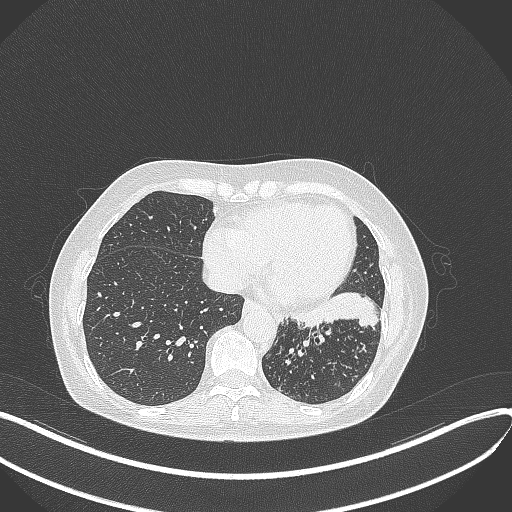
Chest CT, one axial slice. Slice 131 of 429 in the series (ordered by position). Reconstruction kernel B70f. 100 kVp. Lung window (W 1500 / L -600 HU). 1 mm slice thickness. 512 × 512 image matrix. Patient: female, 63 years. Case-level facts recorded for this patient, not image findings: clinical TNM (as recorded): T1b N0 M0; histopathological grade: G2-3.
Structures marked on this image (bounding box drawn by a radiologist):
- lung tumour (recorded histology: adenocarcinoma): bounding box (x1, y1, x2, y2) in pixels: (286, 287, 379, 331)